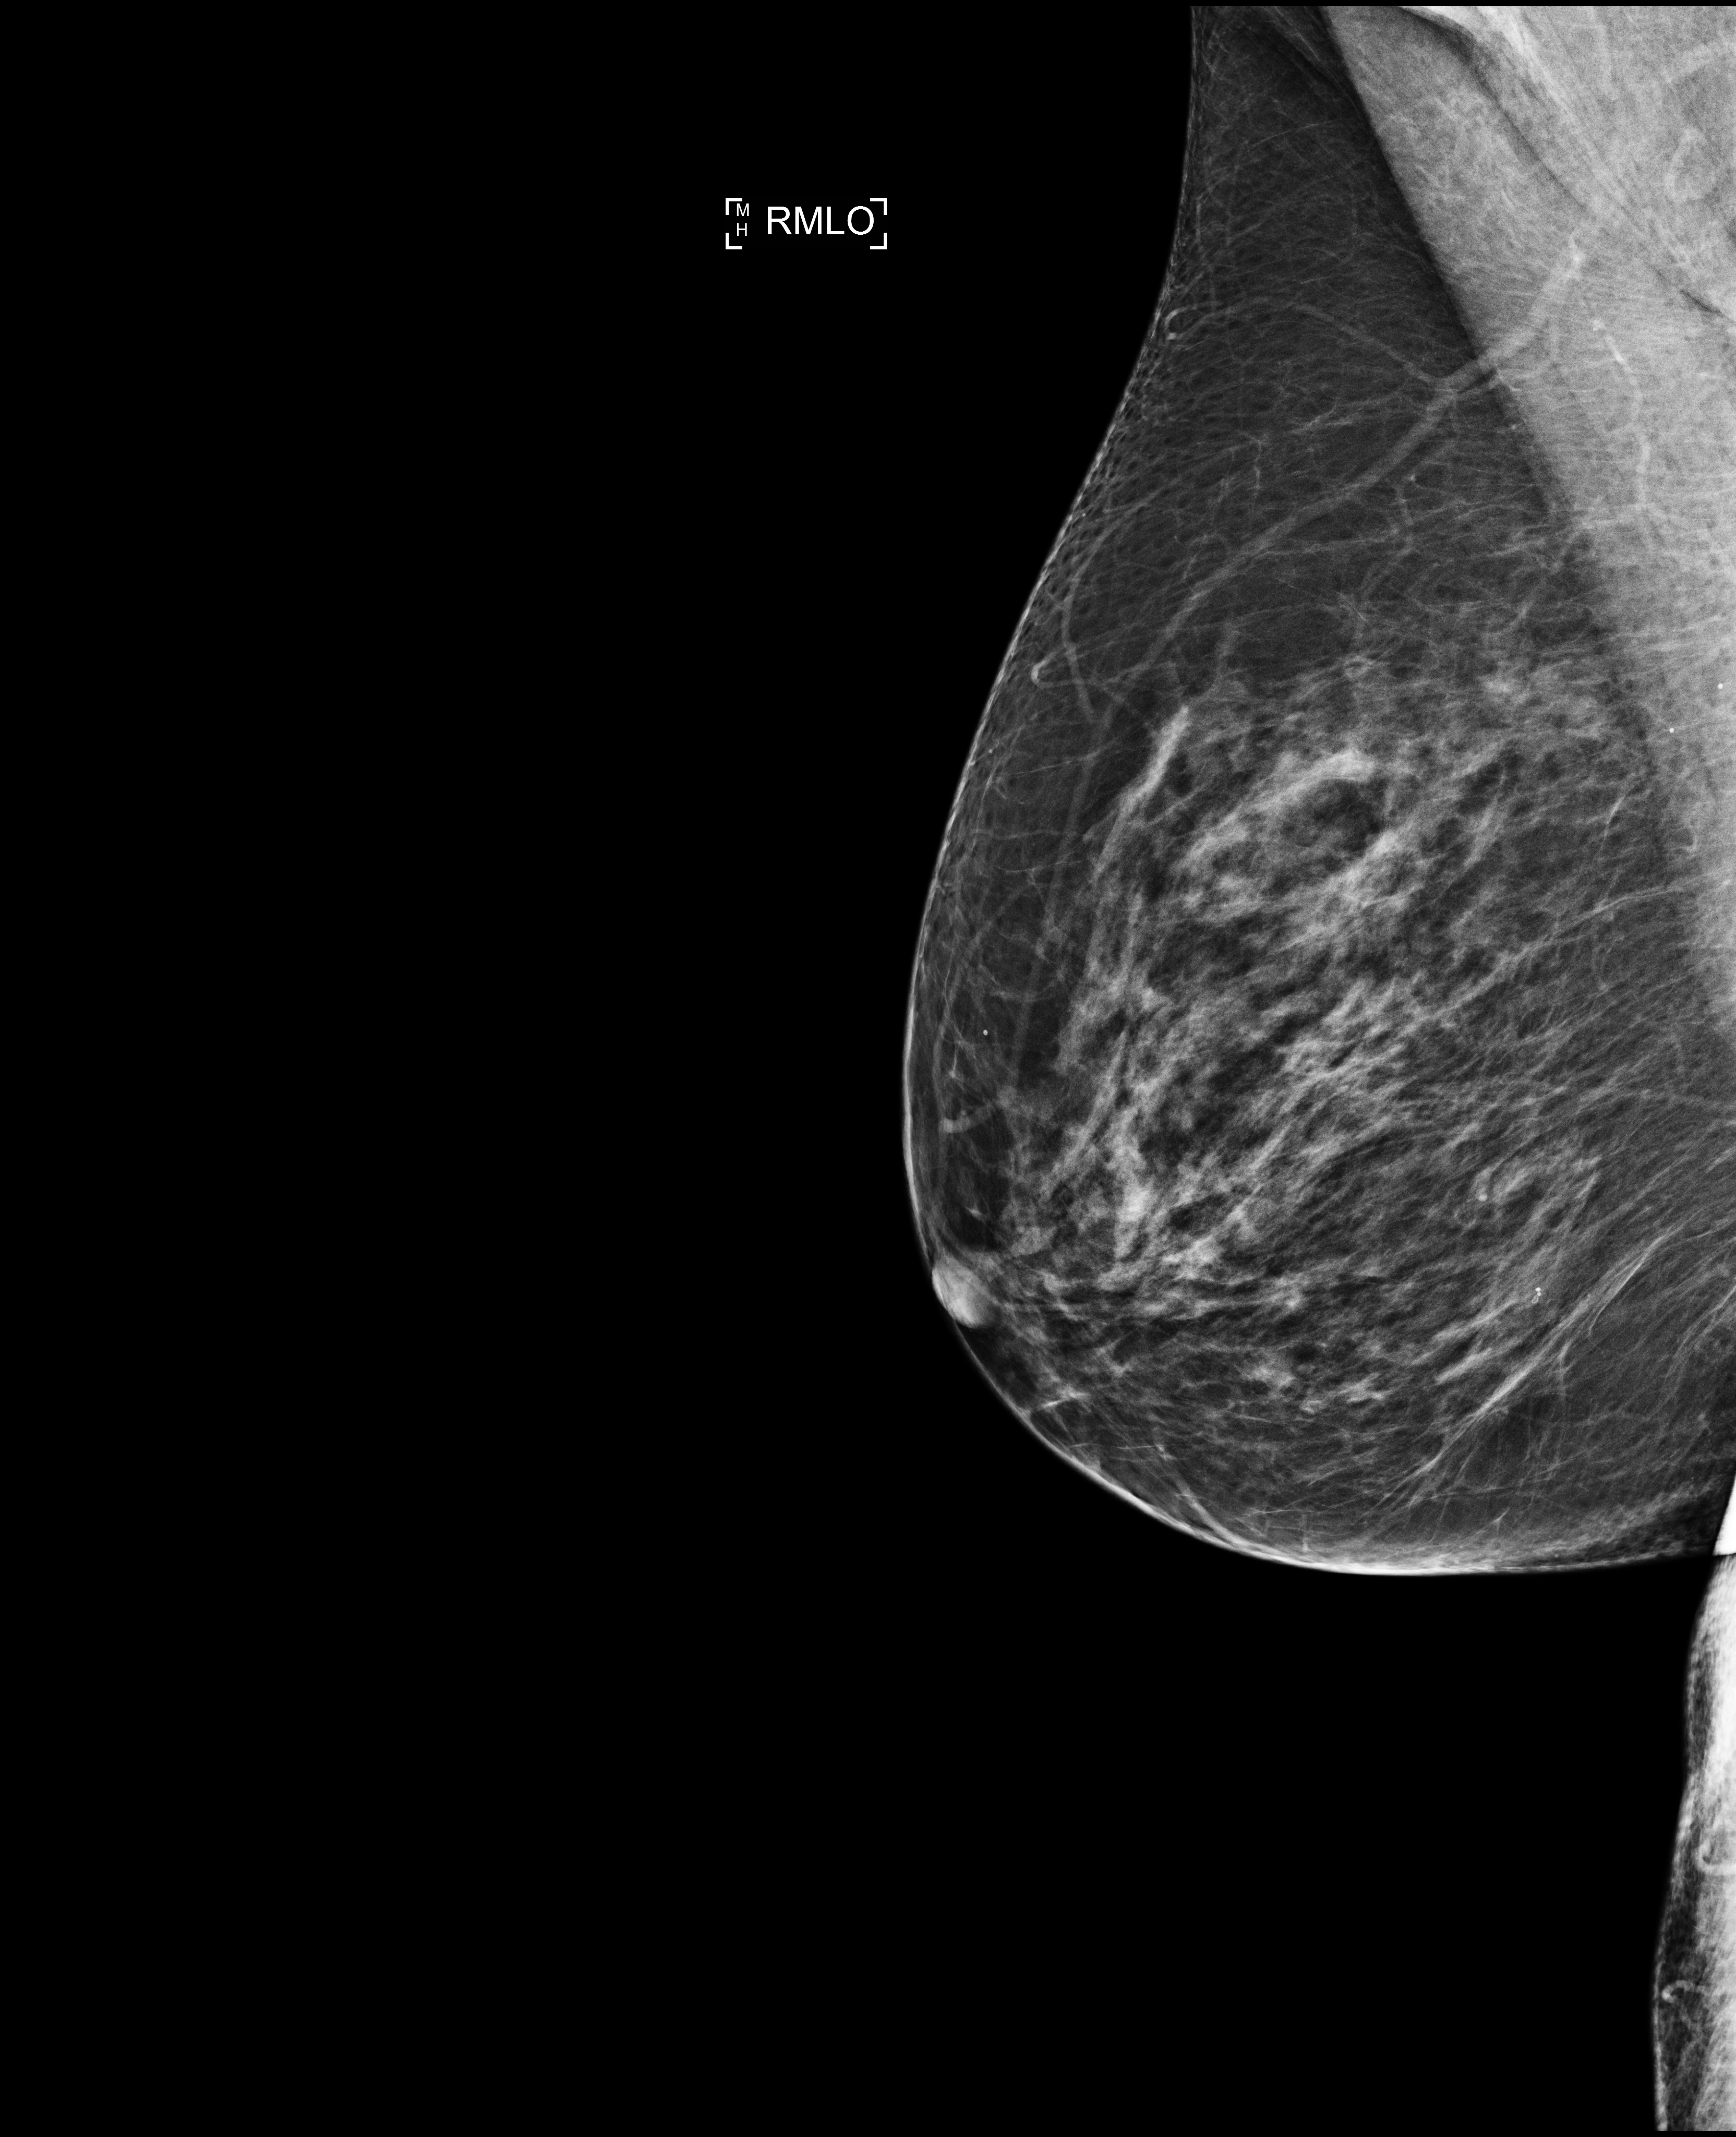
Screening examination, system: Selenia Dimensions. Female patient, age 70 years.
Image type: full-field digital mammogram. Breast: right. Projection: mediolateral oblique (MLO) view.